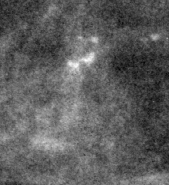
Crop from a digitized film mammogram around one marked abnormality, right breast, CC view.
Finding: calcifications, morphology pleomorphic, distribution clustered; BI-RADS assessment category 4; subtlety rating 3 on a 1 (subtle) to 5 (obvious) scale; pathology result (as recorded, not read from the image): malignant.